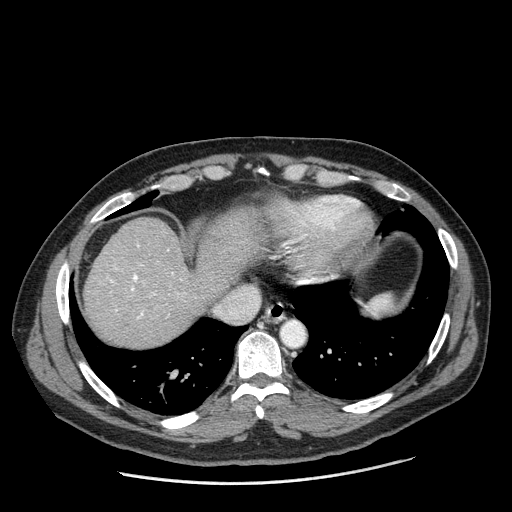
Contrast-enhanced abdominal CT (liver protocol), one axial slice; slice 165 of 198 in the series (ordered by position); reconstruction kernel STANDARD; 120 kVp; one of 2 acquisitions stored at this slice position; soft-tissue window (W 400 / L 40 HU); 2.5 mm slice thickness; 512 × 512 image matrix, field of view 400 × 400 mm. Case-level facts recorded for this patient, not image findings: diagnosis: hepatocellular carcinoma (patient treated with transarterial chemoembolisation; whether this scan precedes or follows treatment is not stated here); TNM stage (as recorded): Stage-II; Child-Pugh class: A; tumour differentiation: moderately differentiated.
Annotated regions visible in this slice (semi-automatic segmentation, software-assisted and operator-edited):
- abdominal aorta: bounding box (x1, y1, x2, y2) in pixels: (283, 322, 304, 345)
- liver parenchyma outside the tumour (the mass and vessels are separate outlines, so this box may not span the whole liver): (84, 210, 260, 346)
- liver vessels: (110, 244, 173, 319)